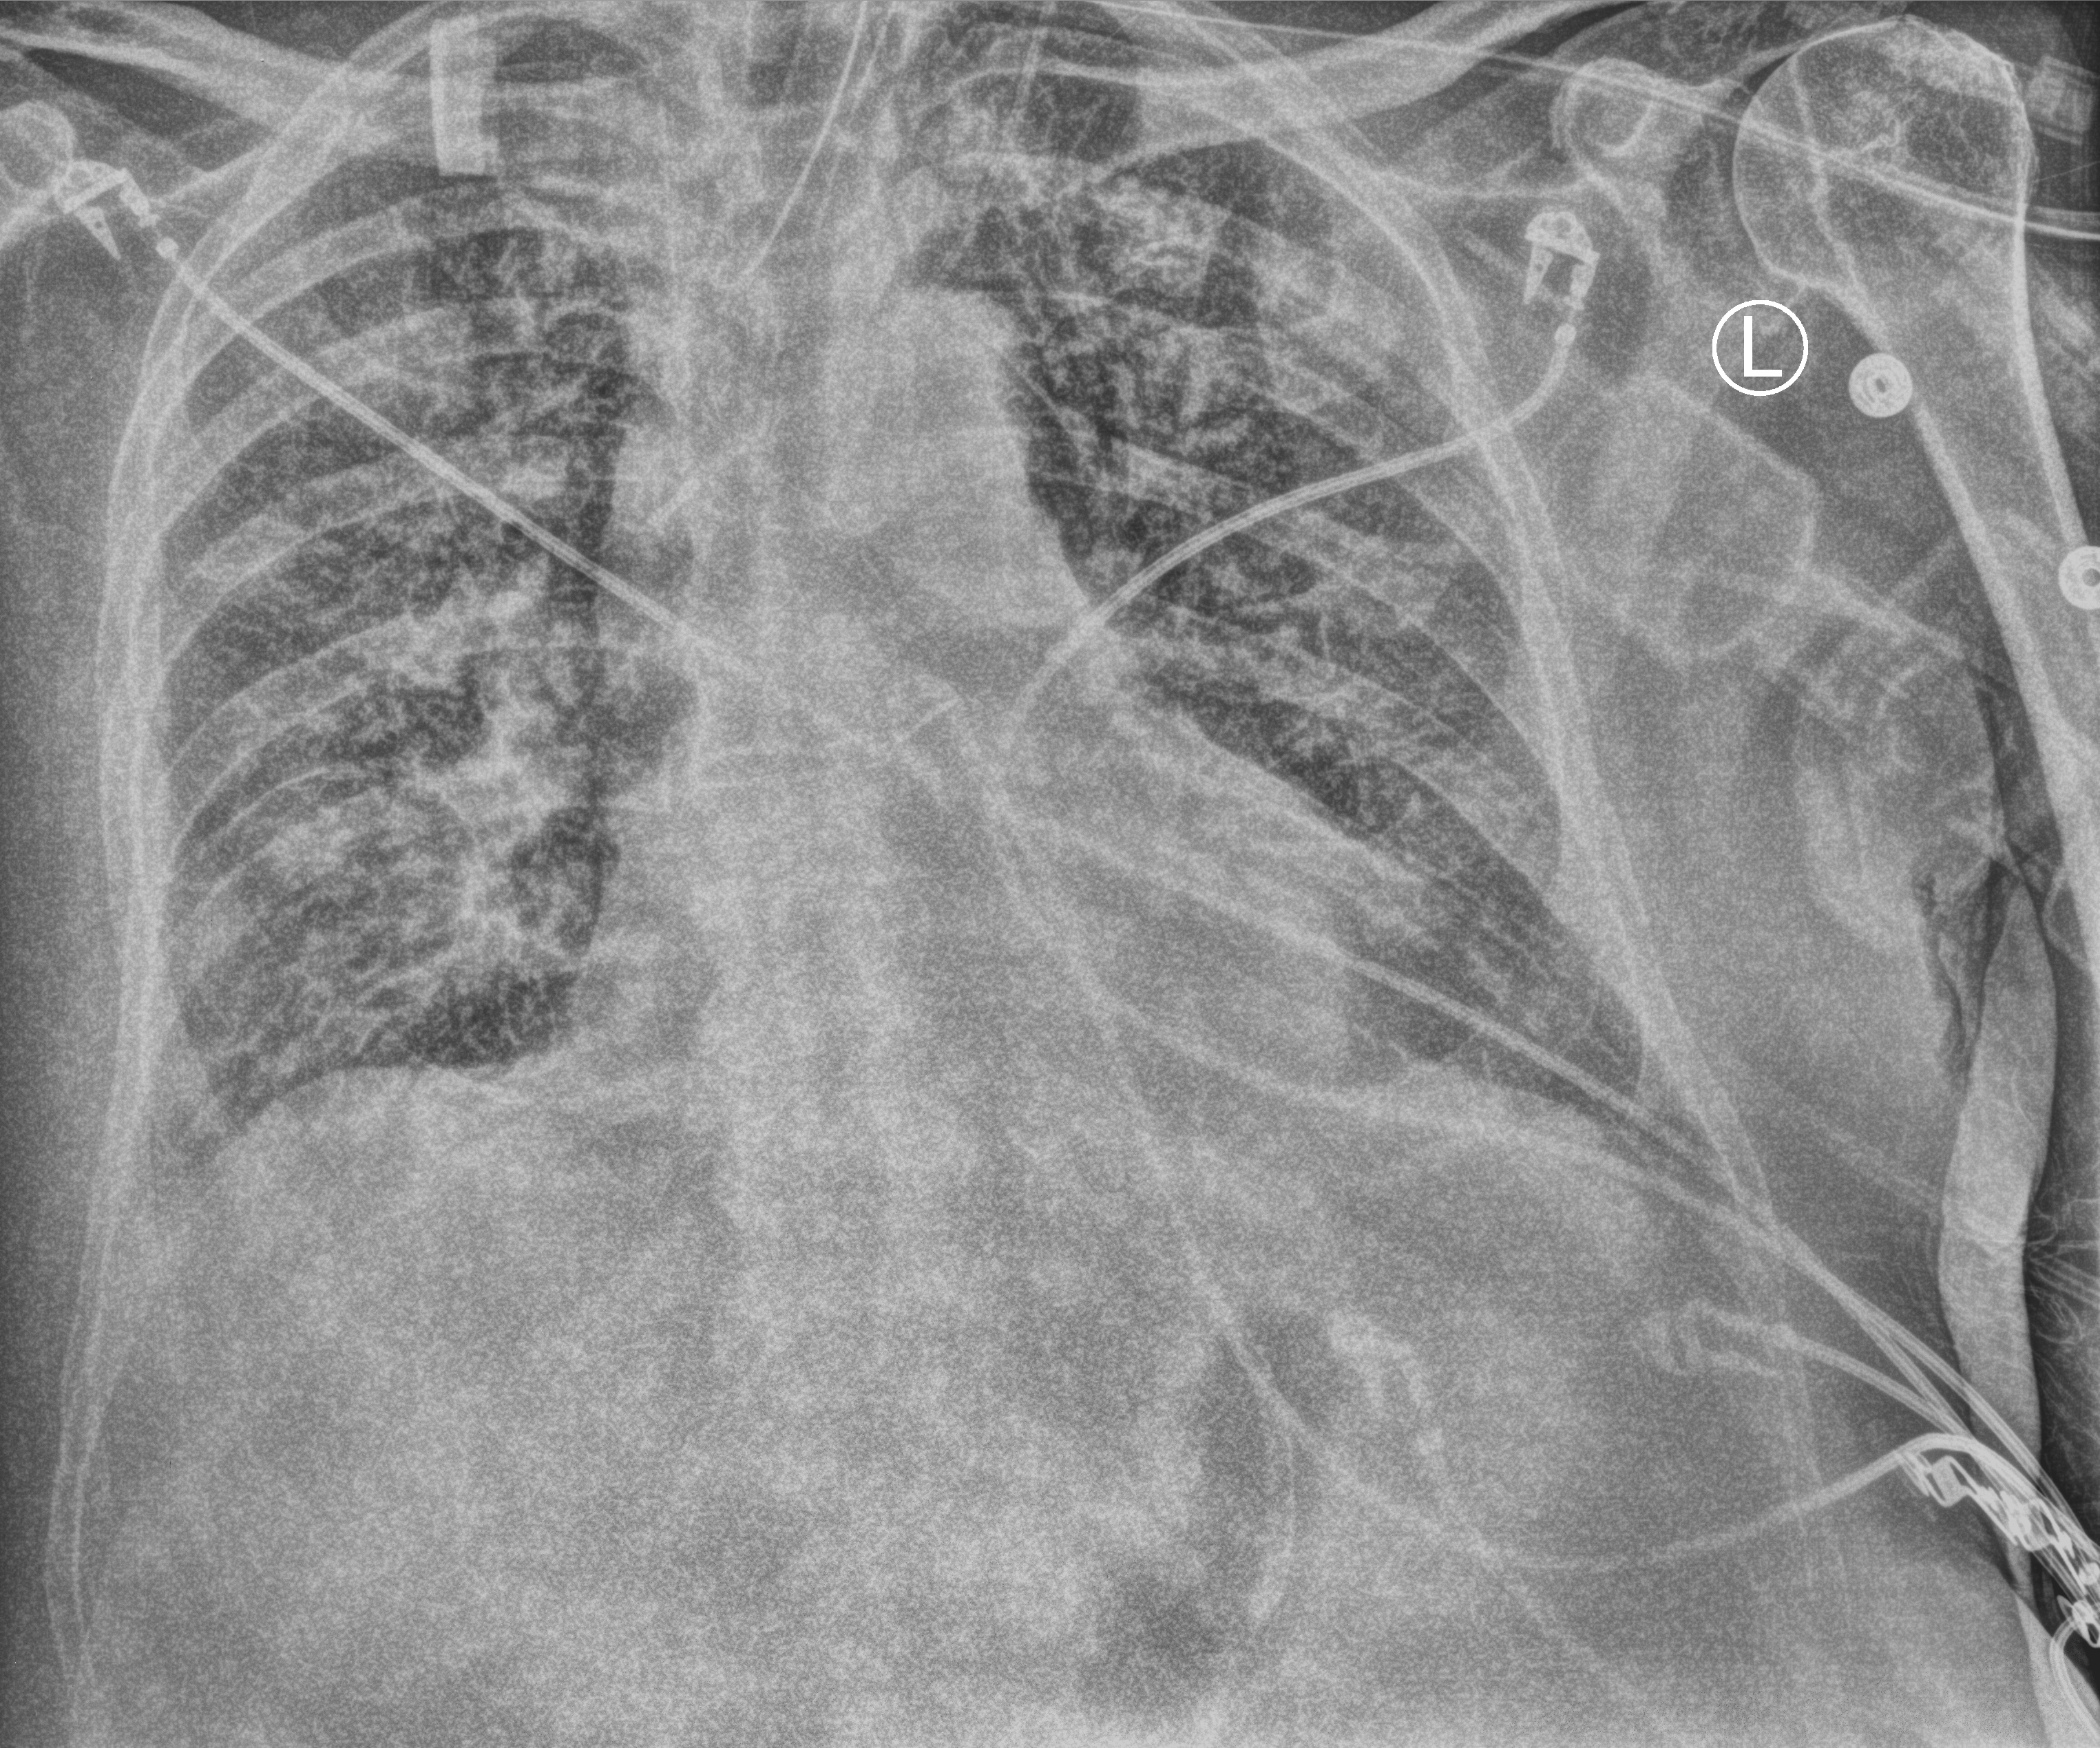
Portable chest radiograph; anteroposterior (AP) projection. Male patient hospitalised with COVID-19, age 75–90 years.
From the hospital-stay record, not from the radiograph (when in the stay this image was taken is not recorded):
- mechanically ventilated during this hospital stay: yes